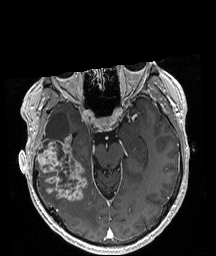
Brain MRI from a brain-tumour surgery series, one axial slice. Position 124 of 208 along the scan axis. T1-weighted post-contrast. 1 mm slice thickness. 216 × 256 image matrix. From the clinical record (not read from this slice): histopathology: Astrocytoma; WHO grade: 4; IDH mutation: yes; tumour location: Right Temporal.
Outlined on this slice (outlined manually by an expert reader):
- tumour: bounding box (x1, y1, x2, y2) in pixels: (36, 134, 88, 201)